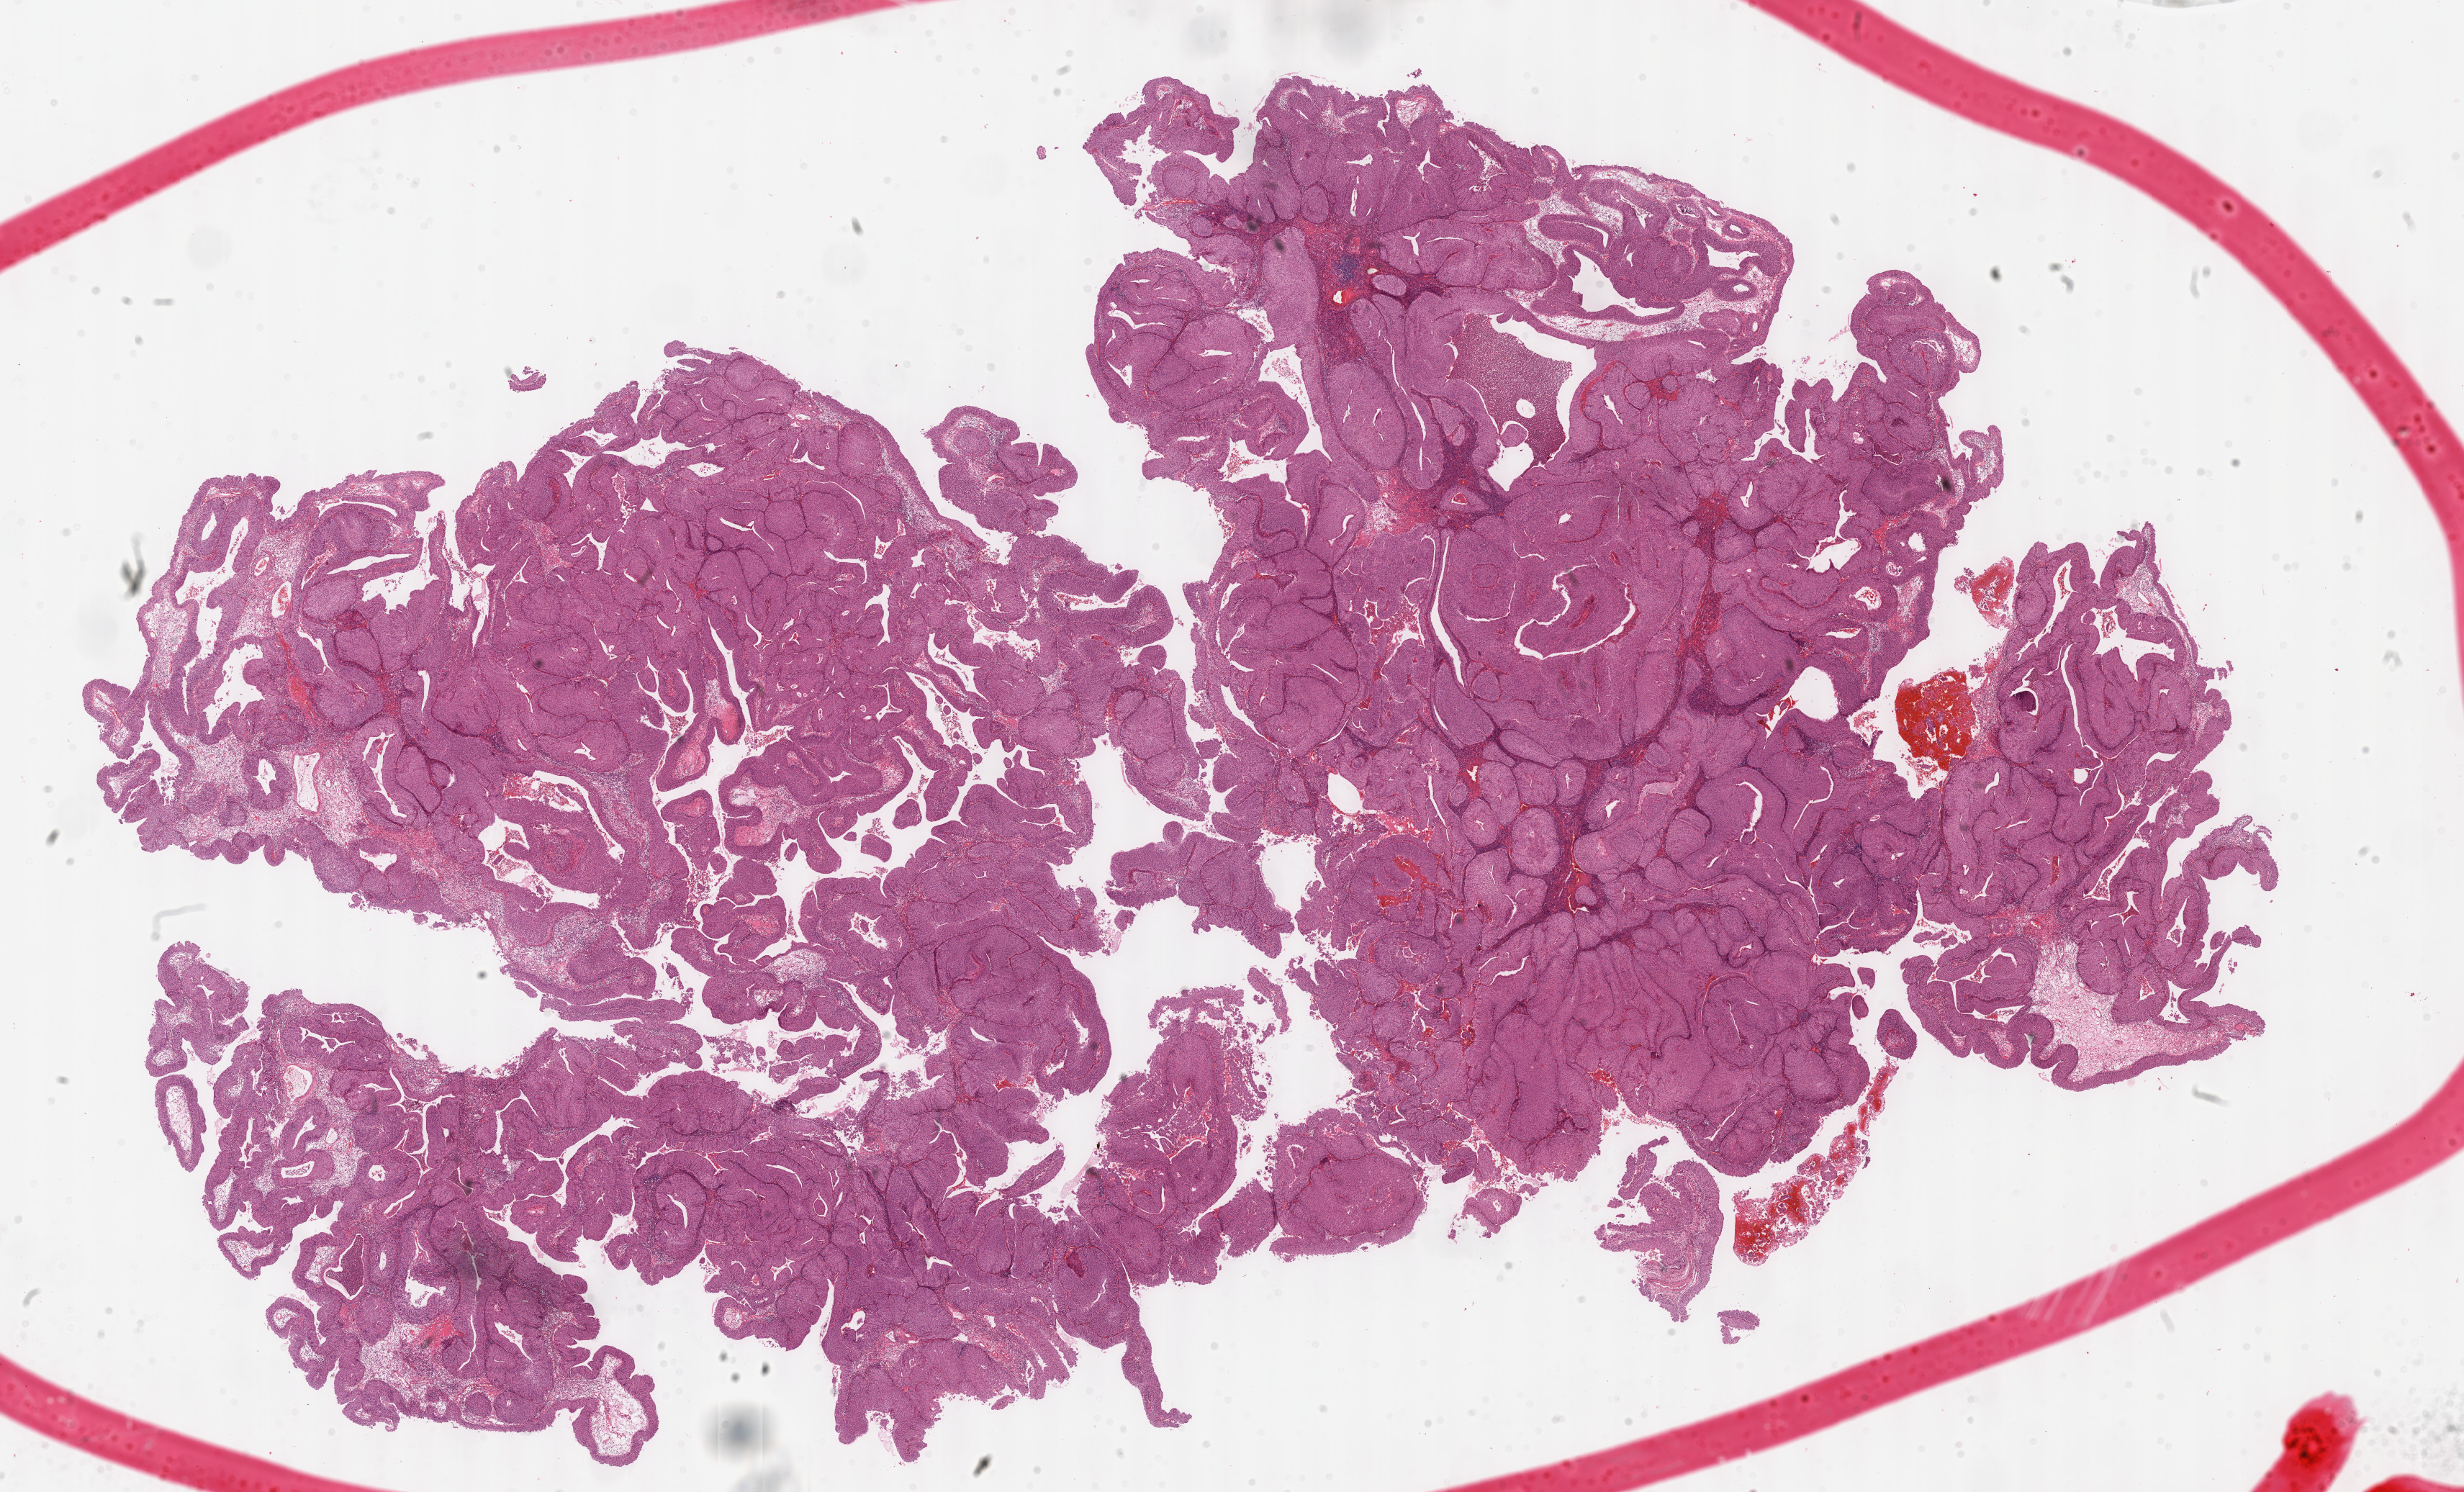
H&E whole-slide image, low-resolution overview of the scanned area, about 27.7 x 16.8 mm (acquisition: 40x scan). FFPE section. Primary tumour sample from the bladder. Male, age 52 years at initial diagnosis.
Pathologic diagnosis: Transitional cell carcinoma.